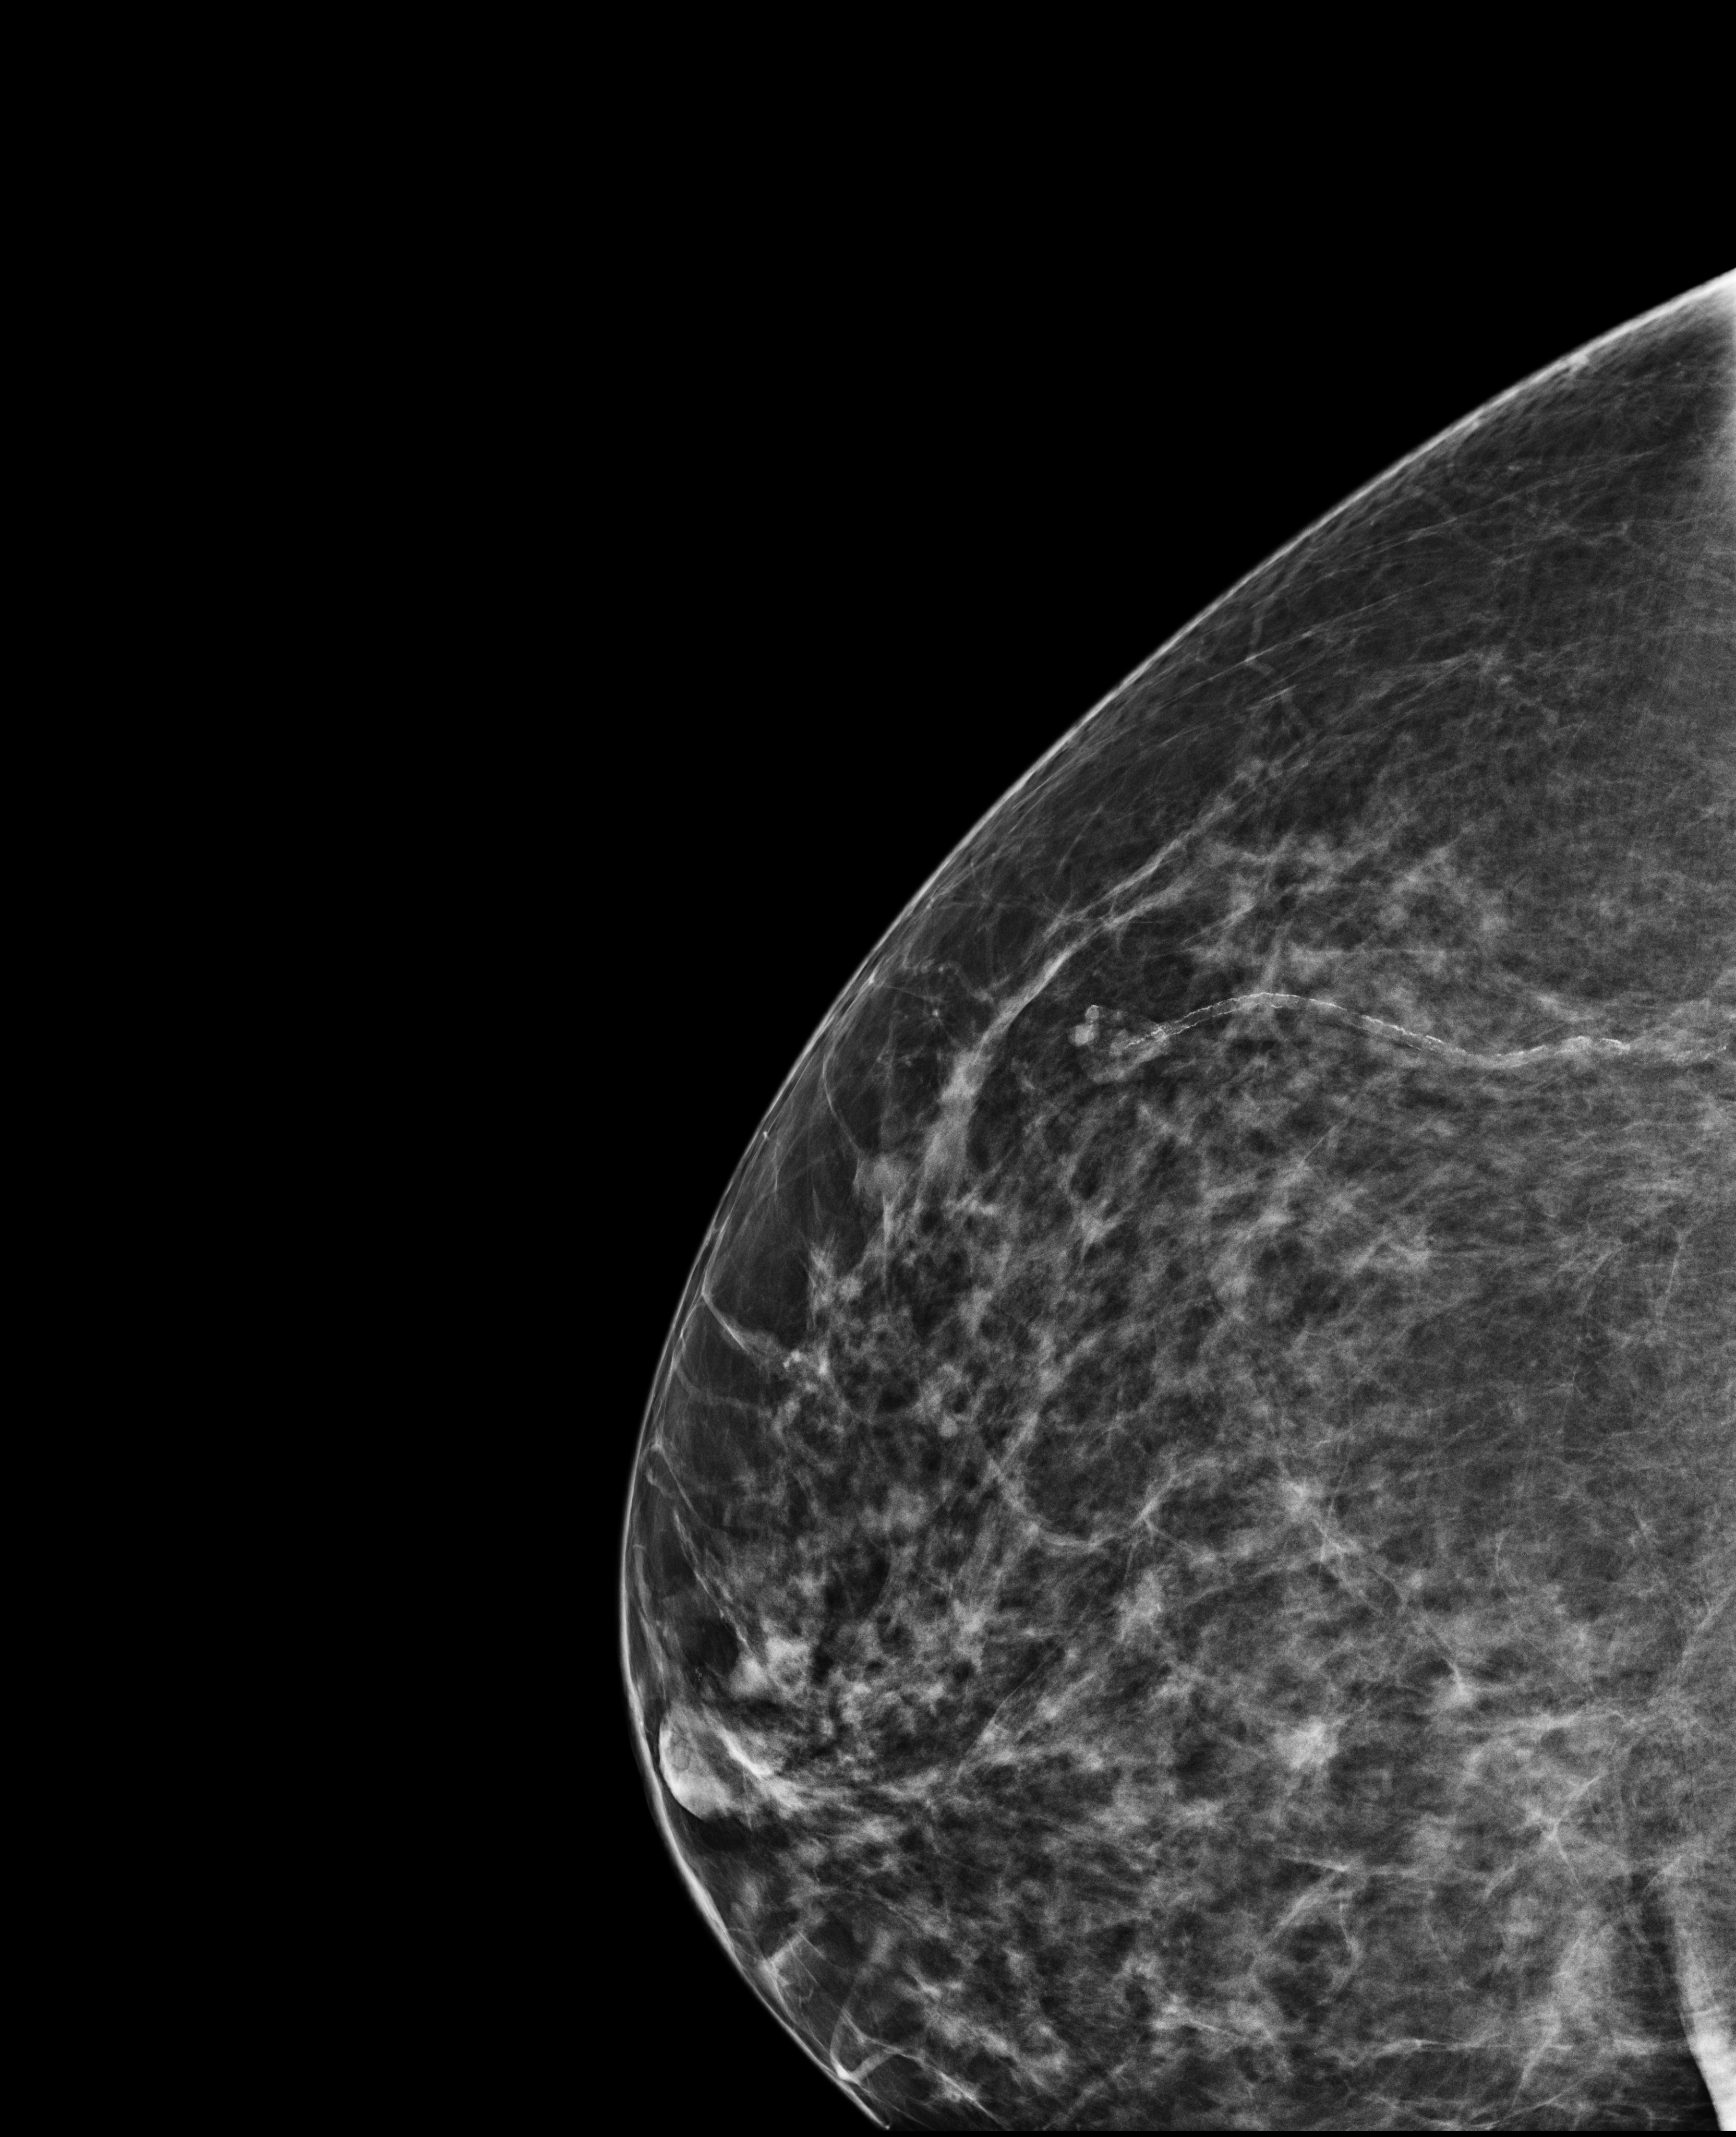
Screening examination, compressed breast thickness 78 mm. Patient aged 68 years (female).
Image type: full-field digital mammogram. Breast: right. Projection: laterally exaggerated craniocaudal (XCCL) view.